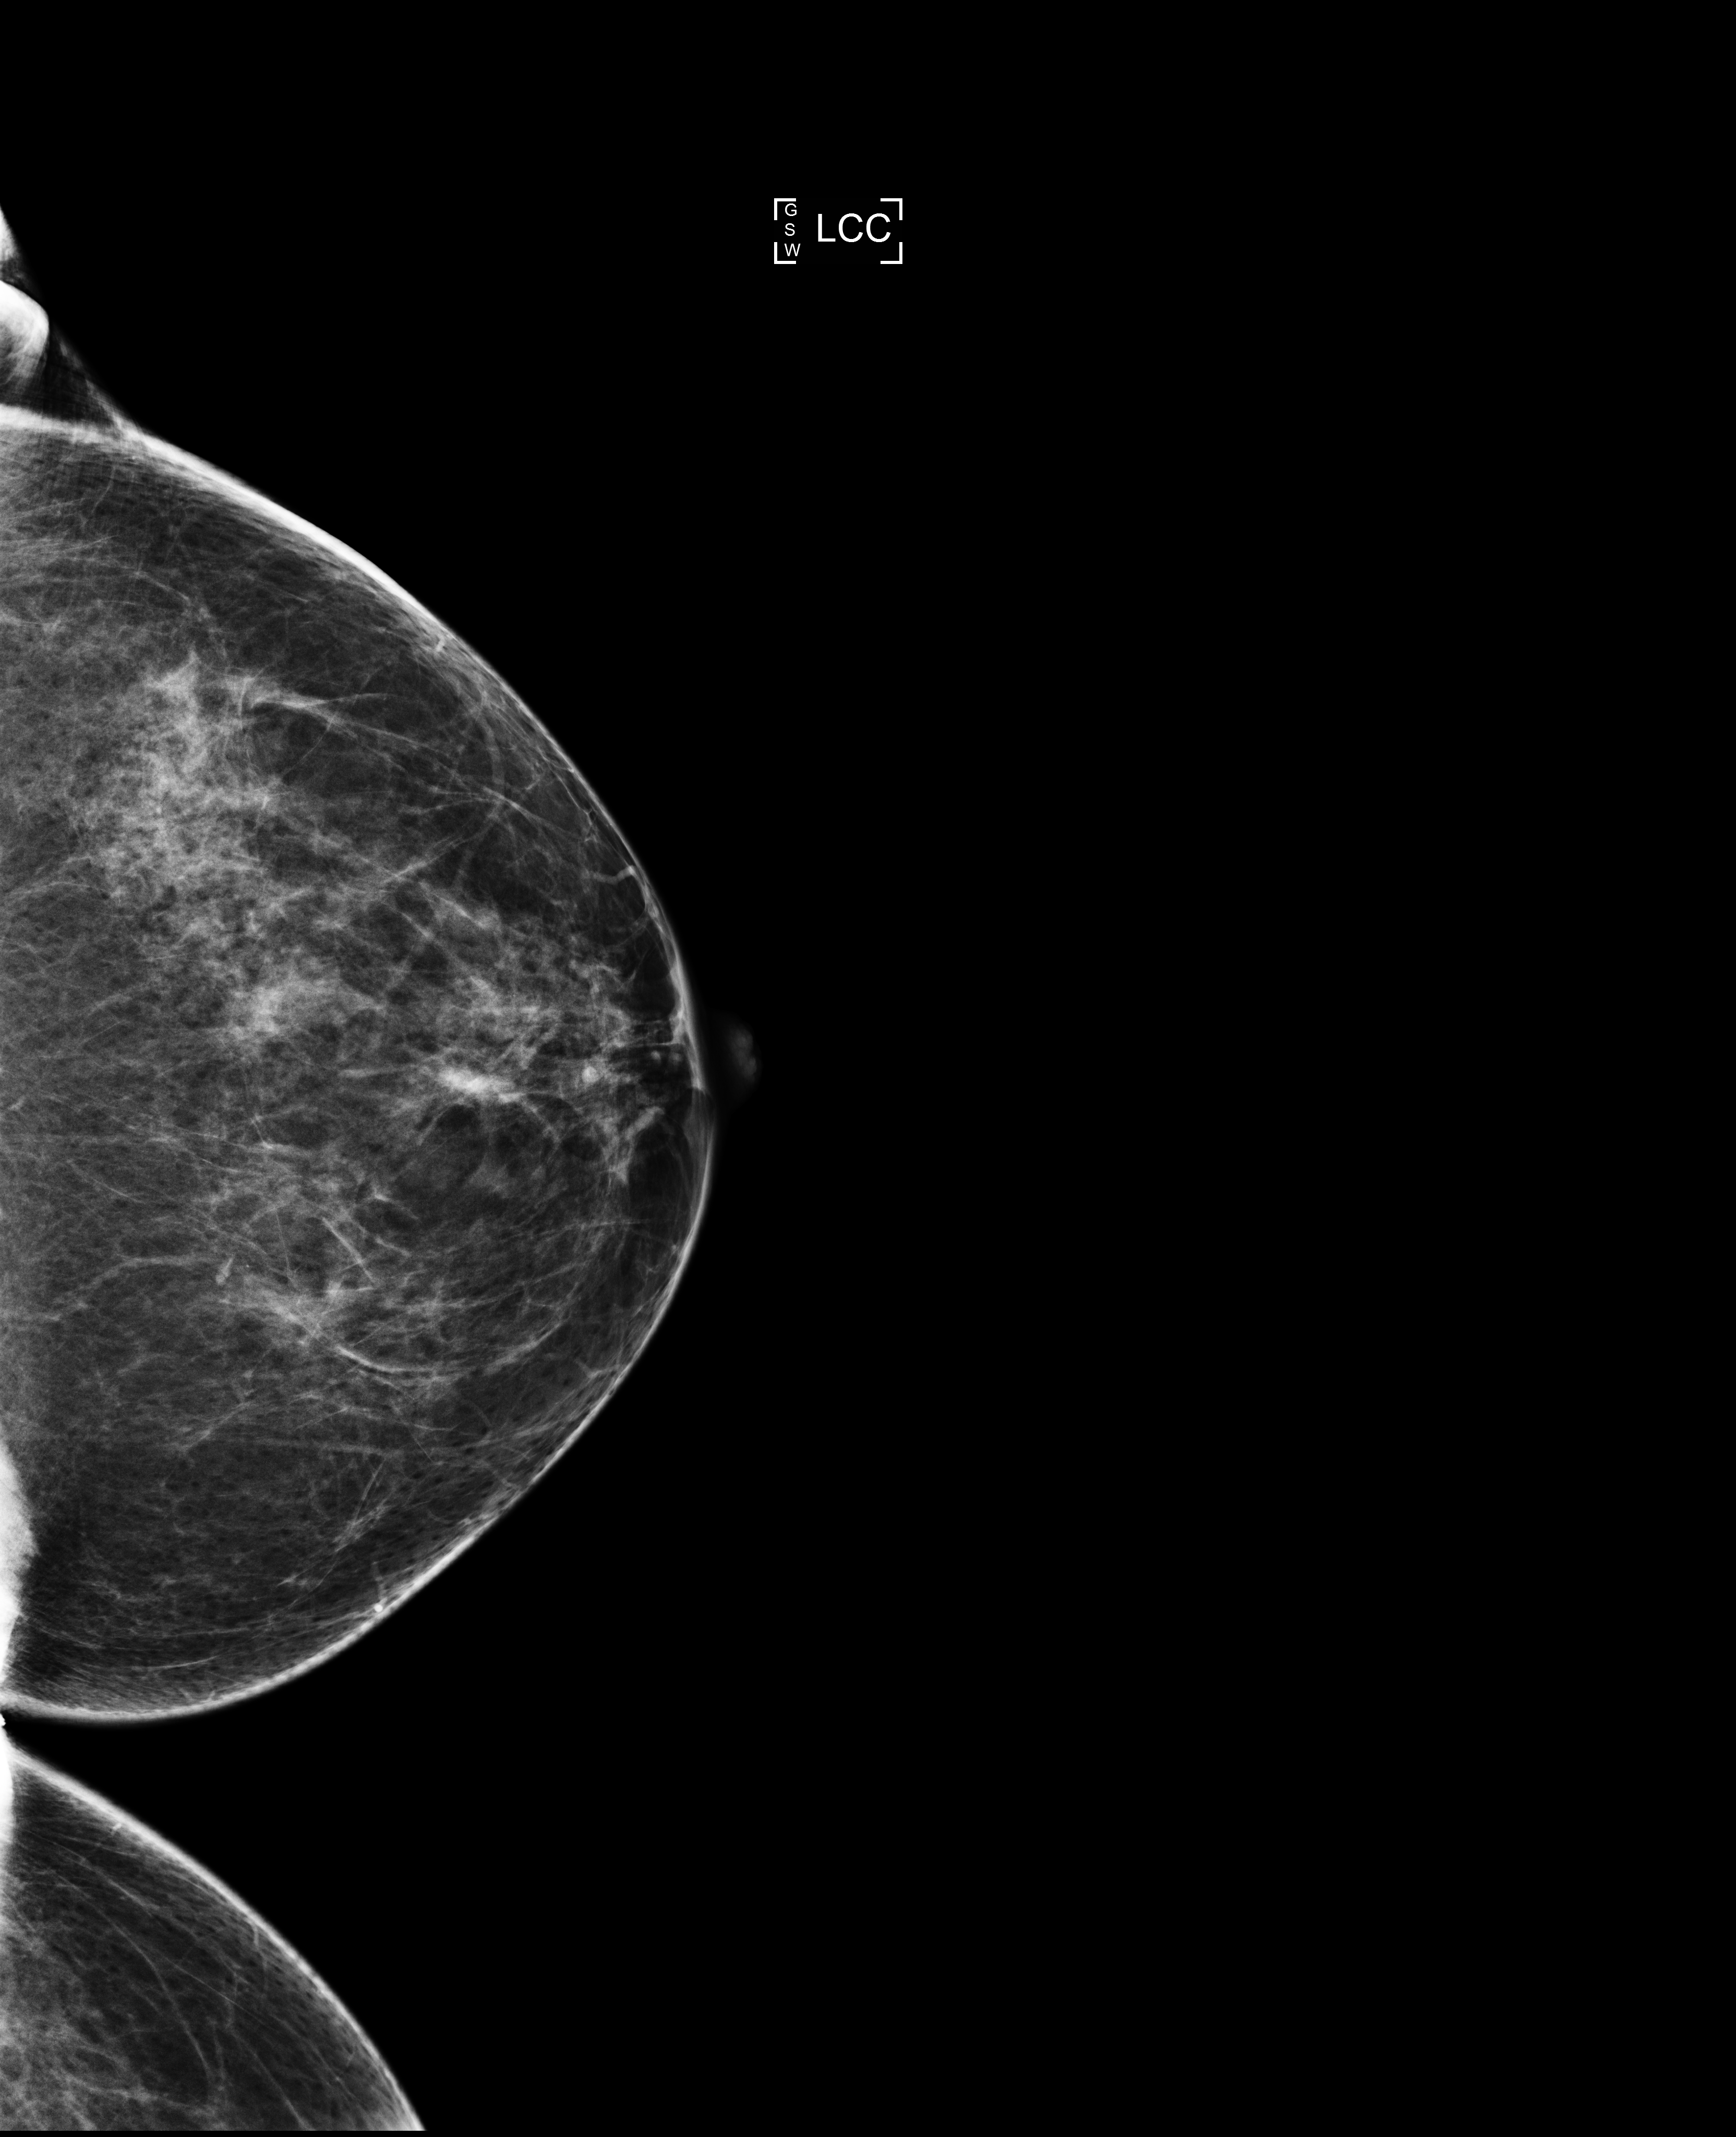
Digital mammogram (FFDM), left breast, CC view, screening examination. Patient: female, 51 years.
Breast density at the screening exam (both breasts): heterogeneously dense (BI-RADS density category c). Final BI-RADS category for the screening round (tomosynthesis exam, both breasts): category 1. Recall: no recall after this screen.